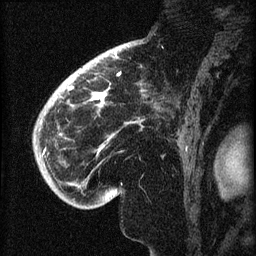
Breast MRI (dynamic contrast-enhanced), one sagittal slice. Slice 49 of 60 in the series (ordered by position). Dynamic contrast-enhanced series, image 2 of 3 at this slice position (ordered by acquisition). 1.5 T. TE 4.2 ms, TR 8.2 ms. 2 mm slice thickness. 256 × 256 image matrix, field of view 180 × 180 mm. Patient: female, 71 years.
Annotated regions visible in this slice (semi-automatic segmentation, software-assisted and operator-edited):
- analysis volume of interest (the breast-tissue region the enhancement analysis was run in; not a lesion): bounding box (x1, y1, x2, y2) in pixels: (40, 72, 147, 196)
- tumour enhancement mask (voxels above the 70 % enhancement threshold inside the analysis volume of interest): (43, 73, 121, 155)